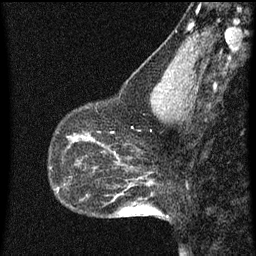
Breast MRI (dynamic contrast-enhanced), one sagittal slice. Slice 20 of 60 in the series (ordered by position). Dynamic contrast-enhanced series, image 2 of 3 at this slice position (ordered by acquisition). 1.5 T. TE 4.2 ms, TR 8 ms. 2 mm slice thickness. 256 × 256 image matrix, field of view 180 × 180 mm. Patient: female, 43 years.
Structures marked on this image (semi-automatic segmentation, software-assisted and operator-edited):
- analysis volume of interest (the breast-tissue region the enhancement analysis was run in; not a lesion): bounding box <53,104,101,151> (left, top, right, bottom; pixels)
- tumour enhancement mask (voxels above the 70 % enhancement threshold inside the analysis volume of interest): <75,140,100,145>